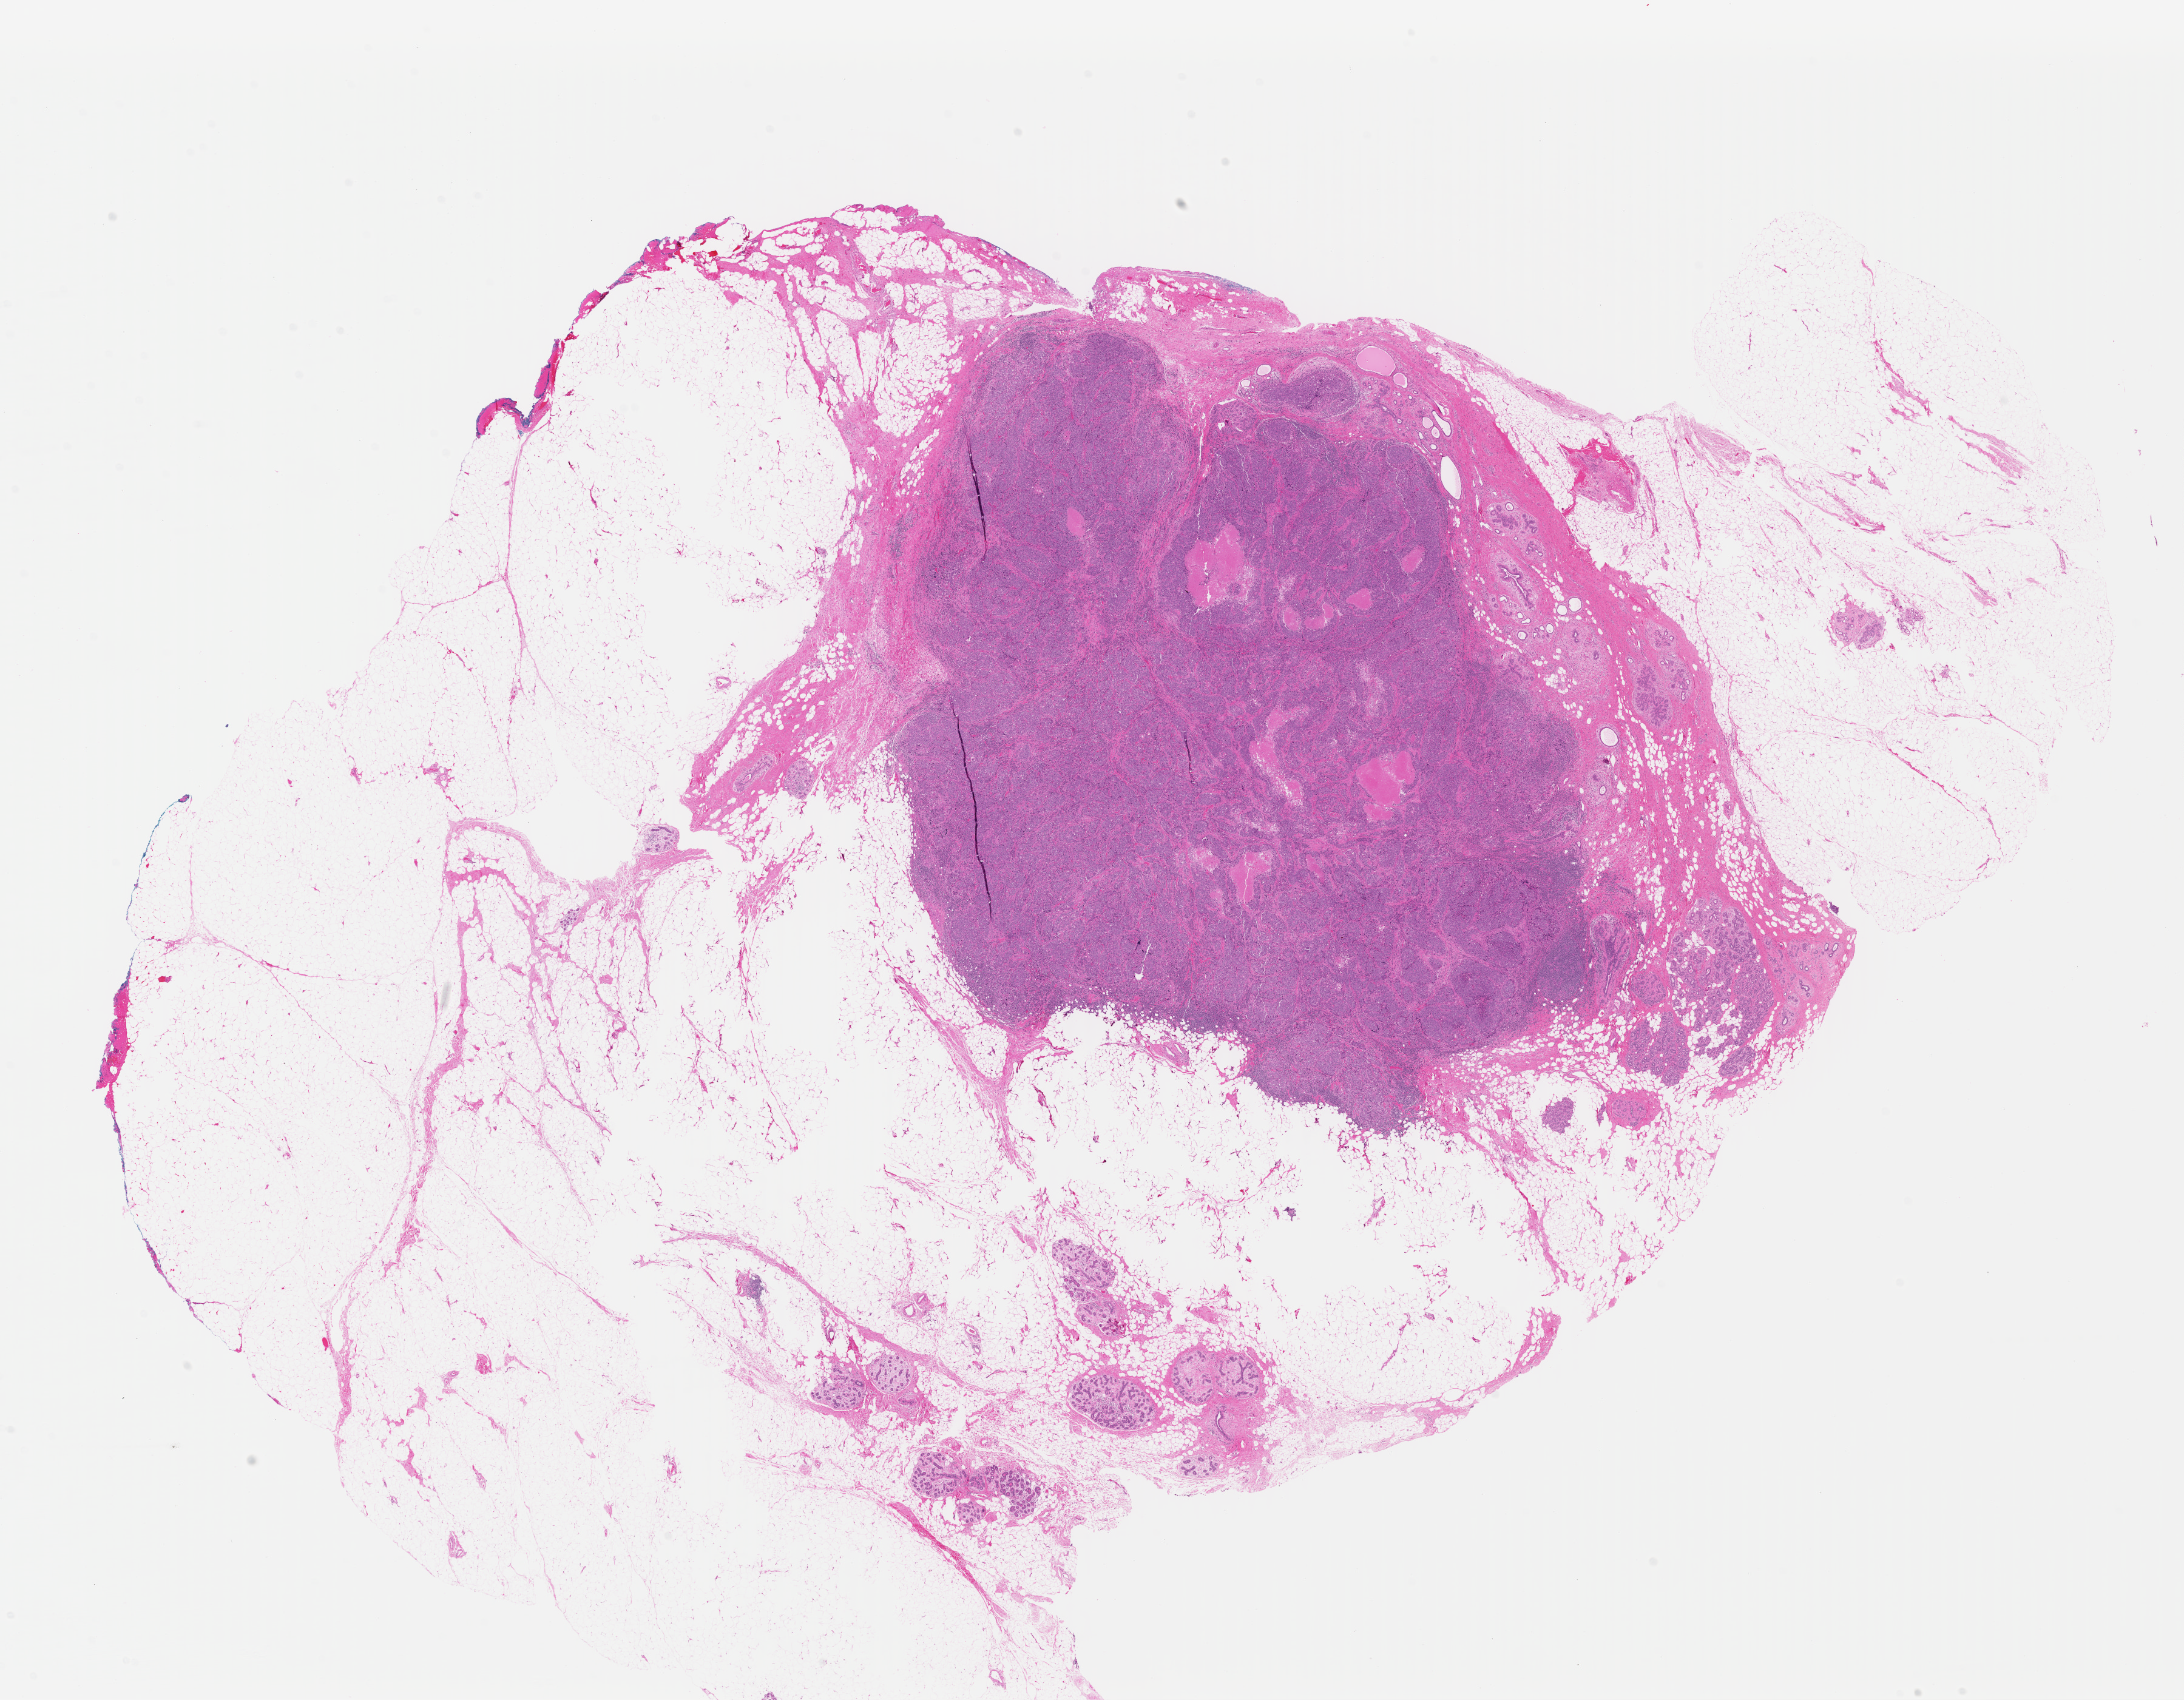
H&E whole-slide image — whole scanned area (about 28.3 x 22.0 mm, acquisition: 40x scan) shown as a low-resolution overview. Formalin-fixed paraffin-embedded (FFPE) diagnostic section. Sample: primary tumour, breast. Female, age 49 years at initial diagnosis.
AJCC pathologic stage: IIA. Histologic diagnosis: Infiltrating duct carcinoma, NOS.